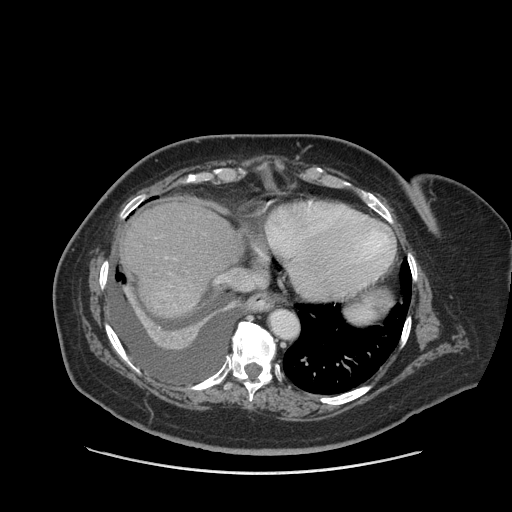
Contrast-enhanced abdominal CT (liver protocol), one axial slice; position 75 of 91 along the scan axis; reconstruction kernel STANDARD; 140 kVp; soft-tissue window (W 400 / L 40 HU); 512 × 512 image matrix. Case-level facts recorded for this patient, not image findings: diagnosis: hepatocellular carcinoma (patient treated with transarterial chemoembolisation; whether this scan precedes or follows treatment is not stated here); TNM stage (as recorded): Stage-I; Child-Pugh class: A.
Structures marked on this image (semi-automatic segmentation, software-assisted and operator-edited):
- abdominal aorta: bounding box (x1, y1, x2, y2) in pixels: (270, 310, 298, 339)
- liver parenchyma outside the tumour (the mass and vessels are separate outlines, so this box may not span the whole liver): (120, 198, 242, 318)